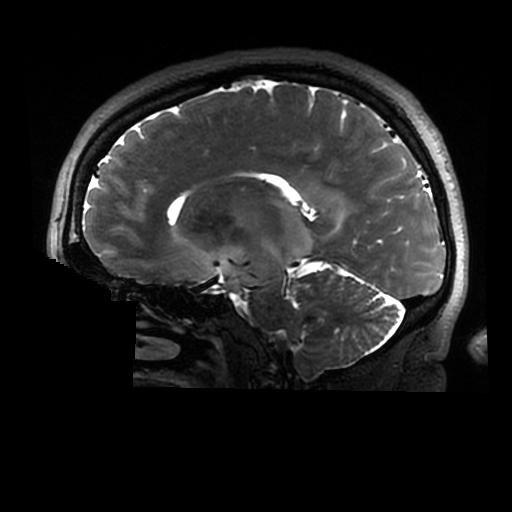
Brain MRI from a brain-tumour surgery series, one sagittal slice; slice 173 of 320 in the series (ordered by position); 512 × 512 image matrix. Case-level facts recorded for this patient, not image findings: histopathology: Astrocytoma; WHO grade: 2; IDH mutation: yes.
Annotated regions visible in this slice (manually delineated by an expert):
- tumour: bounding box (x1, y1, x2, y2) in pixels: (202, 200, 313, 297)